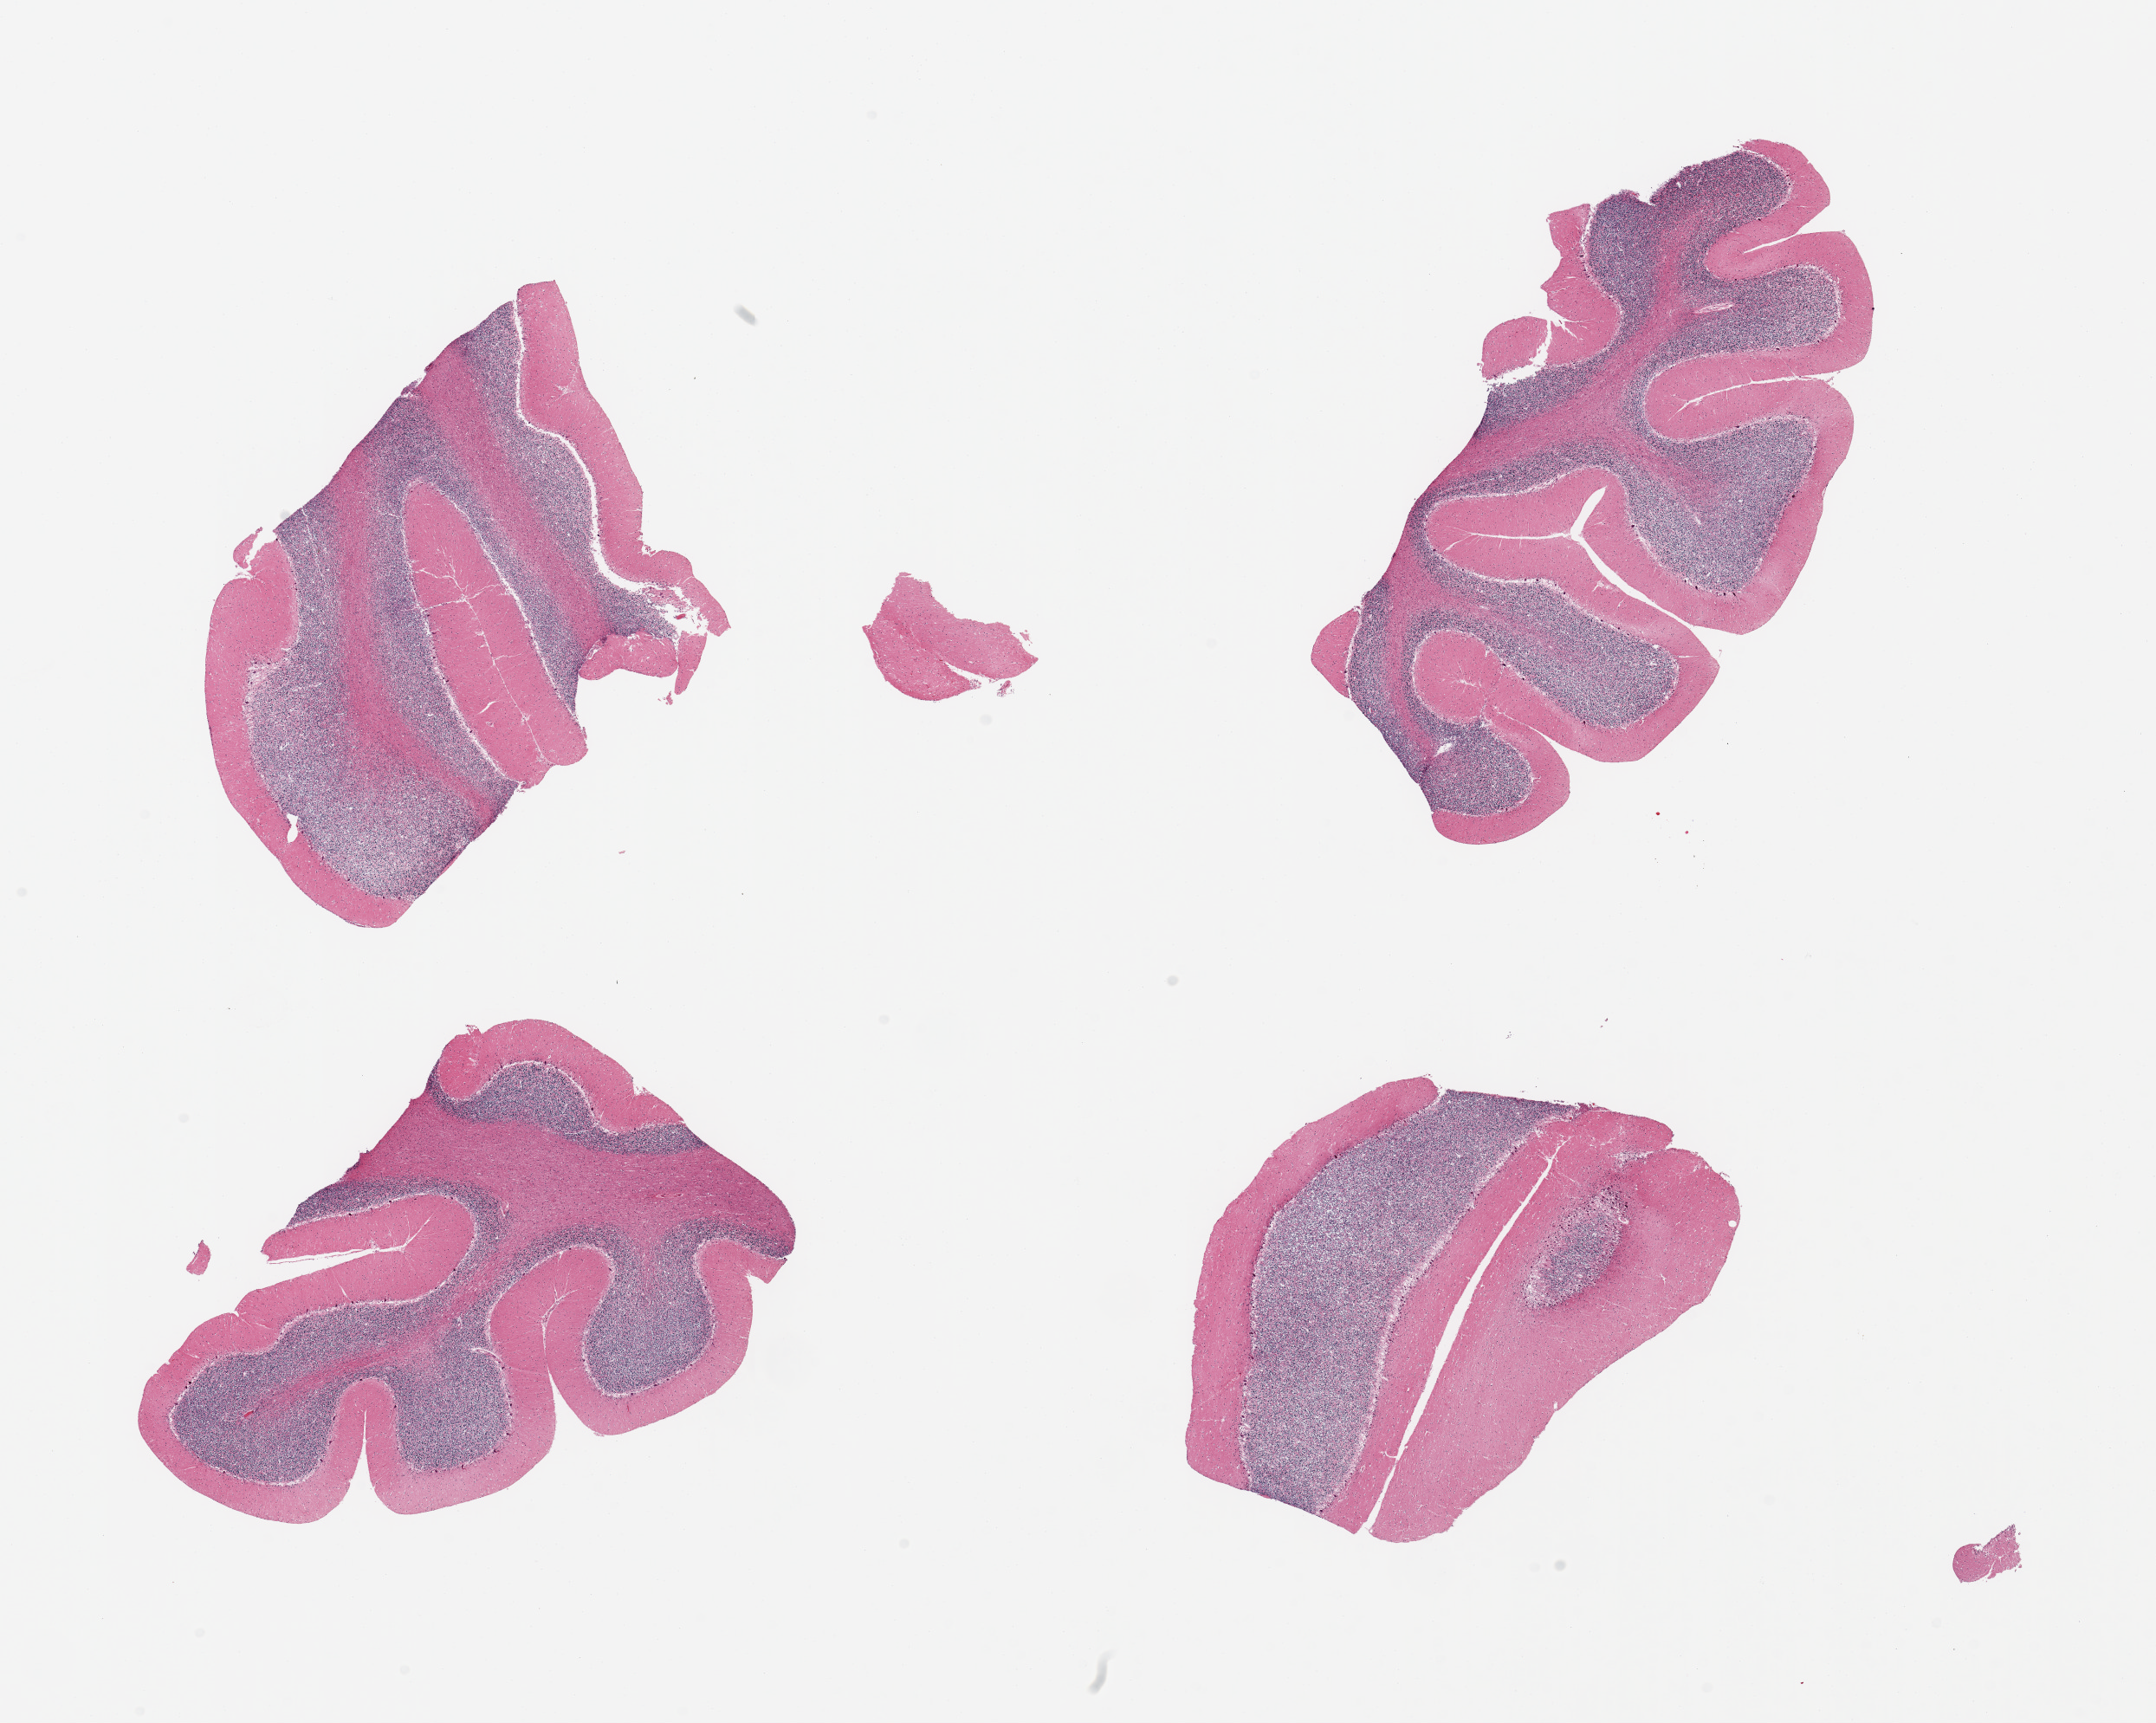
Digitized H&E-stained section, whole scanned area (about 19.7 x 15.7 mm, acquisition: 20x scan) shown as a low-resolution overview. PAXgene-fixed paraffin-embedded (PFPE) section. Target tissue: cerebellum. Tissue donor sample. Female donor.
• reviewer comment on this tissue sample: 4 pieces